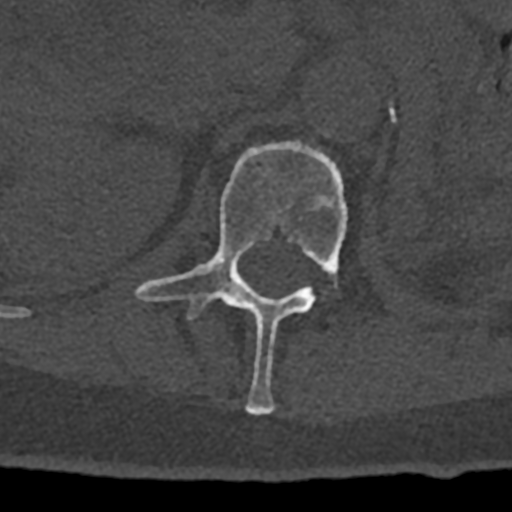
CT including the spine, one axial slice. Slice 432 of 797 in the series (ordered by position). Reconstruction kernel Br40s/3. Bone window (W 1800 / L 400 HU). 0.5 mm slice thickness. 512 × 512 image matrix, field of view 160 × 160 mm. Patient: male, 74 years. From the clinical record (not read from this slice): primary cancer: renal.
Structures marked on this image (semi-automatic segmentation, software-assisted and operator-edited):
- L1 vertebra: box from (x=135, y=140) to (x=348, y=415) px